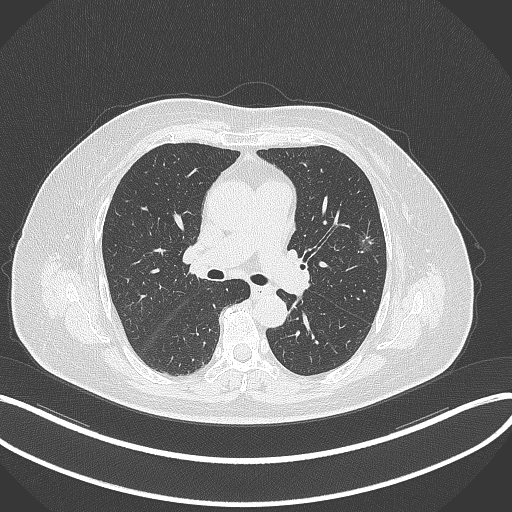
Chest CT, one axial slice; position 215 of 315 along the scan axis; reconstruction kernel B70f; 120 kVp; lung window (W 1500 / L -600 HU); 1 mm slice thickness; 512 × 512 image matrix, field of view 400 × 400 mm. Patient: female, 76 years. Case-level facts recorded for this patient, not image findings: clinical TNM (as recorded): T1b N0 M0; histopathological grade: G1-2.
Structures marked on this image (bounding box drawn by a radiologist):
- lung tumour (recorded histology: adenocarcinoma): bounding box [x1, y1, x2, y2] px = [355, 228, 378, 256]